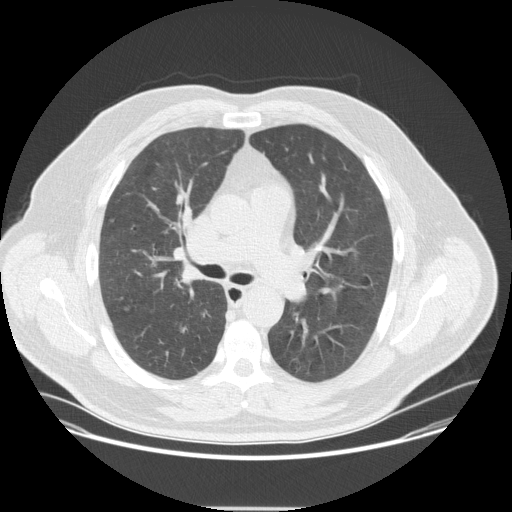
Low-dose screening chest CT, one axial slice; position 221 of 351 along the scan axis; reconstruction kernel STANDARD; 120 kVp; lung window (W 1500 / L -600 HU); 2.5 mm slice thickness; 512 × 512 image matrix, field of view 419 × 419 mm.
Annotated regions visible in this slice (manually delineated by an expert):
- lesion 1 (tumor, upper lobe of right lung): box from (x=181, y=272) to (x=198, y=285) px